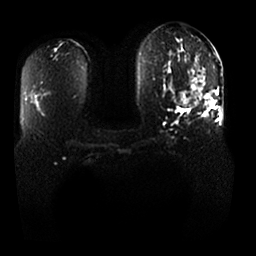
Breast MRI, one axial slice. Position 12 of 25 along the scan axis. Diffusion-weighted series; image 2 of 4 stored at this slice position (different b-values; order by instance number). 1.5 T. 4 mm slice thickness. 256 × 256 image matrix. Female patient.
Annotated regions visible in this slice (outlined manually by an expert reader):
- tumour on diffusion-weighted imaging: bounding box (x1, y1, x2, y2) in pixels: (177, 67, 214, 108)